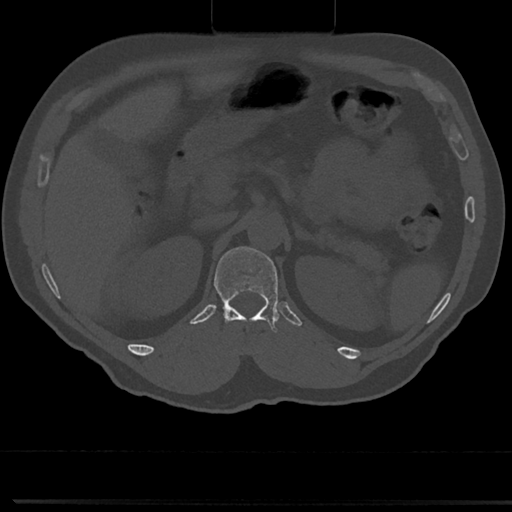
CT including the spine, one axial slice; slice 142 of 817 in the series (ordered by position); reconstruction kernel Br40s/3; bone window (W 1800 / L 400 HU); 0.5 mm slice thickness; 512 × 512 image matrix. Male patient, age 61 years. Case-level facts recorded for this patient, not image findings: primary cancer: prostate.
Structures marked on this image (semi-automatic segmentation, software-assisted and operator-edited):
- T12 vertebra: bounding box <211,247,281,355> (left, top, right, bottom; pixels)